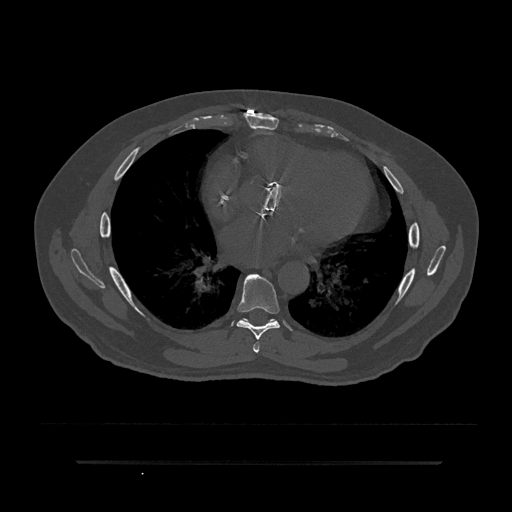
CT including the spine, one axial slice. Reconstruction kernel Br40s/3. 120 kVp. Bone window (W 1800 / L 400 HU). 512 × 512 image matrix, field of view 464 × 464 mm. Male patient, age 59 years. From the clinical record (not read from this slice): primary cancer: bile ducts; vertebrae with lytic lesions (as recorded): T10.
Outlined on this slice (semi-automatically segmented with operator editing):
- T6 vertebra: bounding box (x1, y1, x2, y2) in pixels: (253, 342, 260, 353)
- T7 vertebra: (236, 274, 280, 340)
- T8 vertebra: (241, 318, 248, 322)